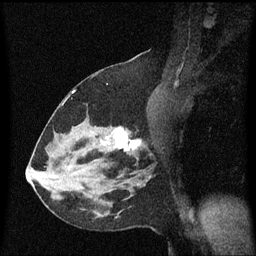
Breast MRI (dynamic contrast-enhanced), one sagittal slice. Position 36 of 60 along the scan axis. Dynamic contrast-enhanced series, image 2 of 3 at this slice position (ordered by acquisition). 1.5 T. TE 4.2 ms, TR 8.4 ms. 2 mm slice thickness. 256 × 256 image matrix, field of view 200 × 200 mm. Female patient, age 37 years. From the clinical record (not read from this slice): setting: breast cancer imaged before/during neoadjuvant chemotherapy; receptor status: HR-positive, HER2-negative.
Structures marked on this image (semi-automatically segmented with operator editing):
- analysis volume of interest (the breast-tissue region the enhancement analysis was run in; not a lesion): bounding box (x1, y1, x2, y2) in pixels: (95, 126, 154, 171)
- tumour enhancement mask (voxels above the 70 % enhancement threshold inside the analysis volume of interest): (102, 128, 142, 151)